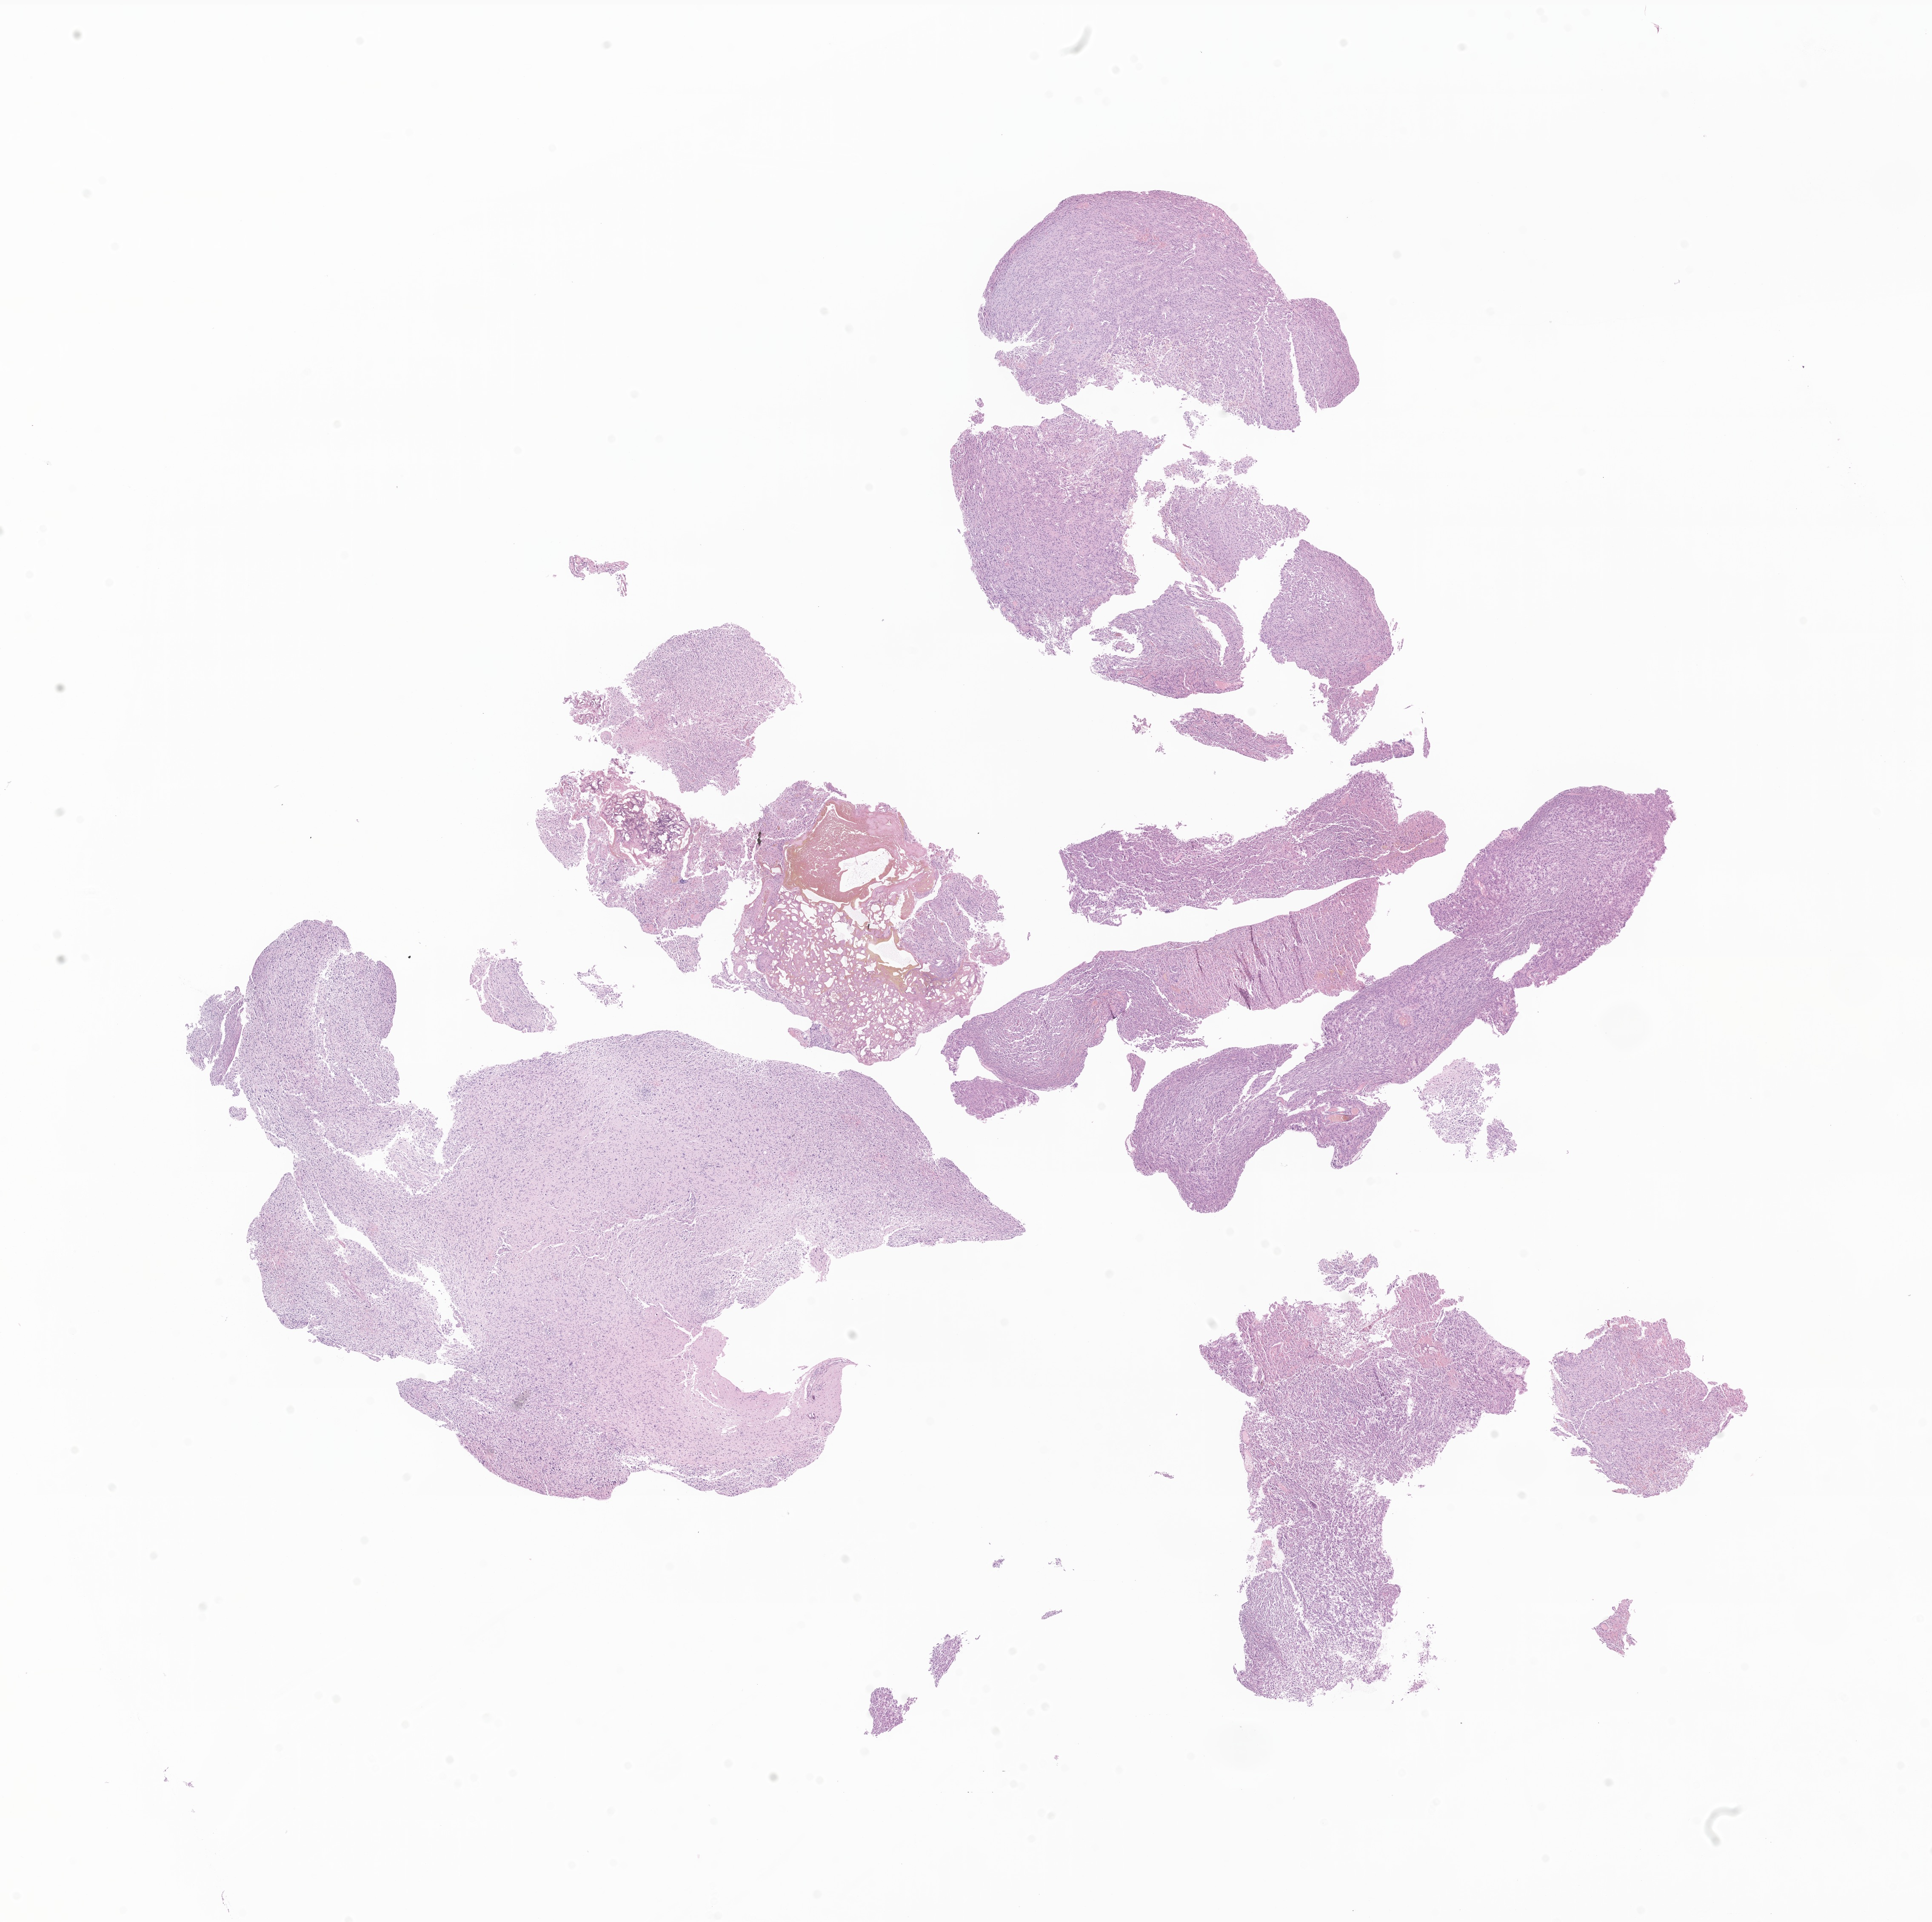
Hematoxylin and eosin (H&E) whole-slide image of tumor tissue from the frontal lobe — shown as a low-resolution overview of the whole scanned area (about 19.1 x 19.0 mm); formalin-fixed, paraffin-embedded (FFPE) tissue. Patient male; age 191 months (15 years 11 months).
Diagnosis (ICD-O-3 morphology term): Pleomorphic xanthoastrocytoma, NOS.